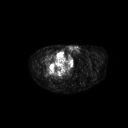
FDG PET of an extremity soft-tissue mass (from a PET/CT study), one axial slice; position 277 of 311 along the scan axis; 3.27 mm slice thickness; 128 × 128 image matrix, field of view 700 × 700 mm. Patient: male, 50 years. Case-level facts recorded for this patient, not image findings: histological type: undifferentiated - pleiomorphic; grade: high; site of the primary tumour: right thigh.
Structures marked on this image (expert contour drawn on MRI and transferred to this co-registered scan by the dataset authors):
- gross tumour volume including surrounding oedema: bounding box <48,50,66,68> (left, top, right, bottom; pixels)
- gross tumour volume (mass): <48,50,66,68>